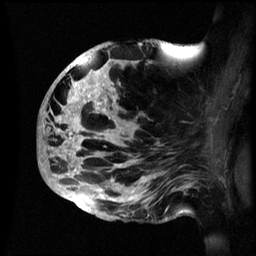
Breast MRI (dynamic contrast-enhanced), one sagittal slice. Slice 31 of 60 in the series (ordered by position). Dynamic contrast-enhanced series, image 2 of 3 at this slice position (ordered by acquisition). 1.5 T. TE 4.2 ms, TR 8.4 ms. 2.4 mm slice thickness. 256 × 256 image matrix, field of view 230 × 230 mm. Patient: female, 48 years.
Structures marked on this image (semi-automatic segmentation, software-assisted and operator-edited):
- analysis volume of interest (the breast-tissue region the enhancement analysis was run in; not a lesion): box from (x=39, y=41) to (x=195, y=222) px
- tumour enhancement mask (voxels above the 70 % enhancement threshold inside the analysis volume of interest): (x=39, y=43)–(x=171, y=212)